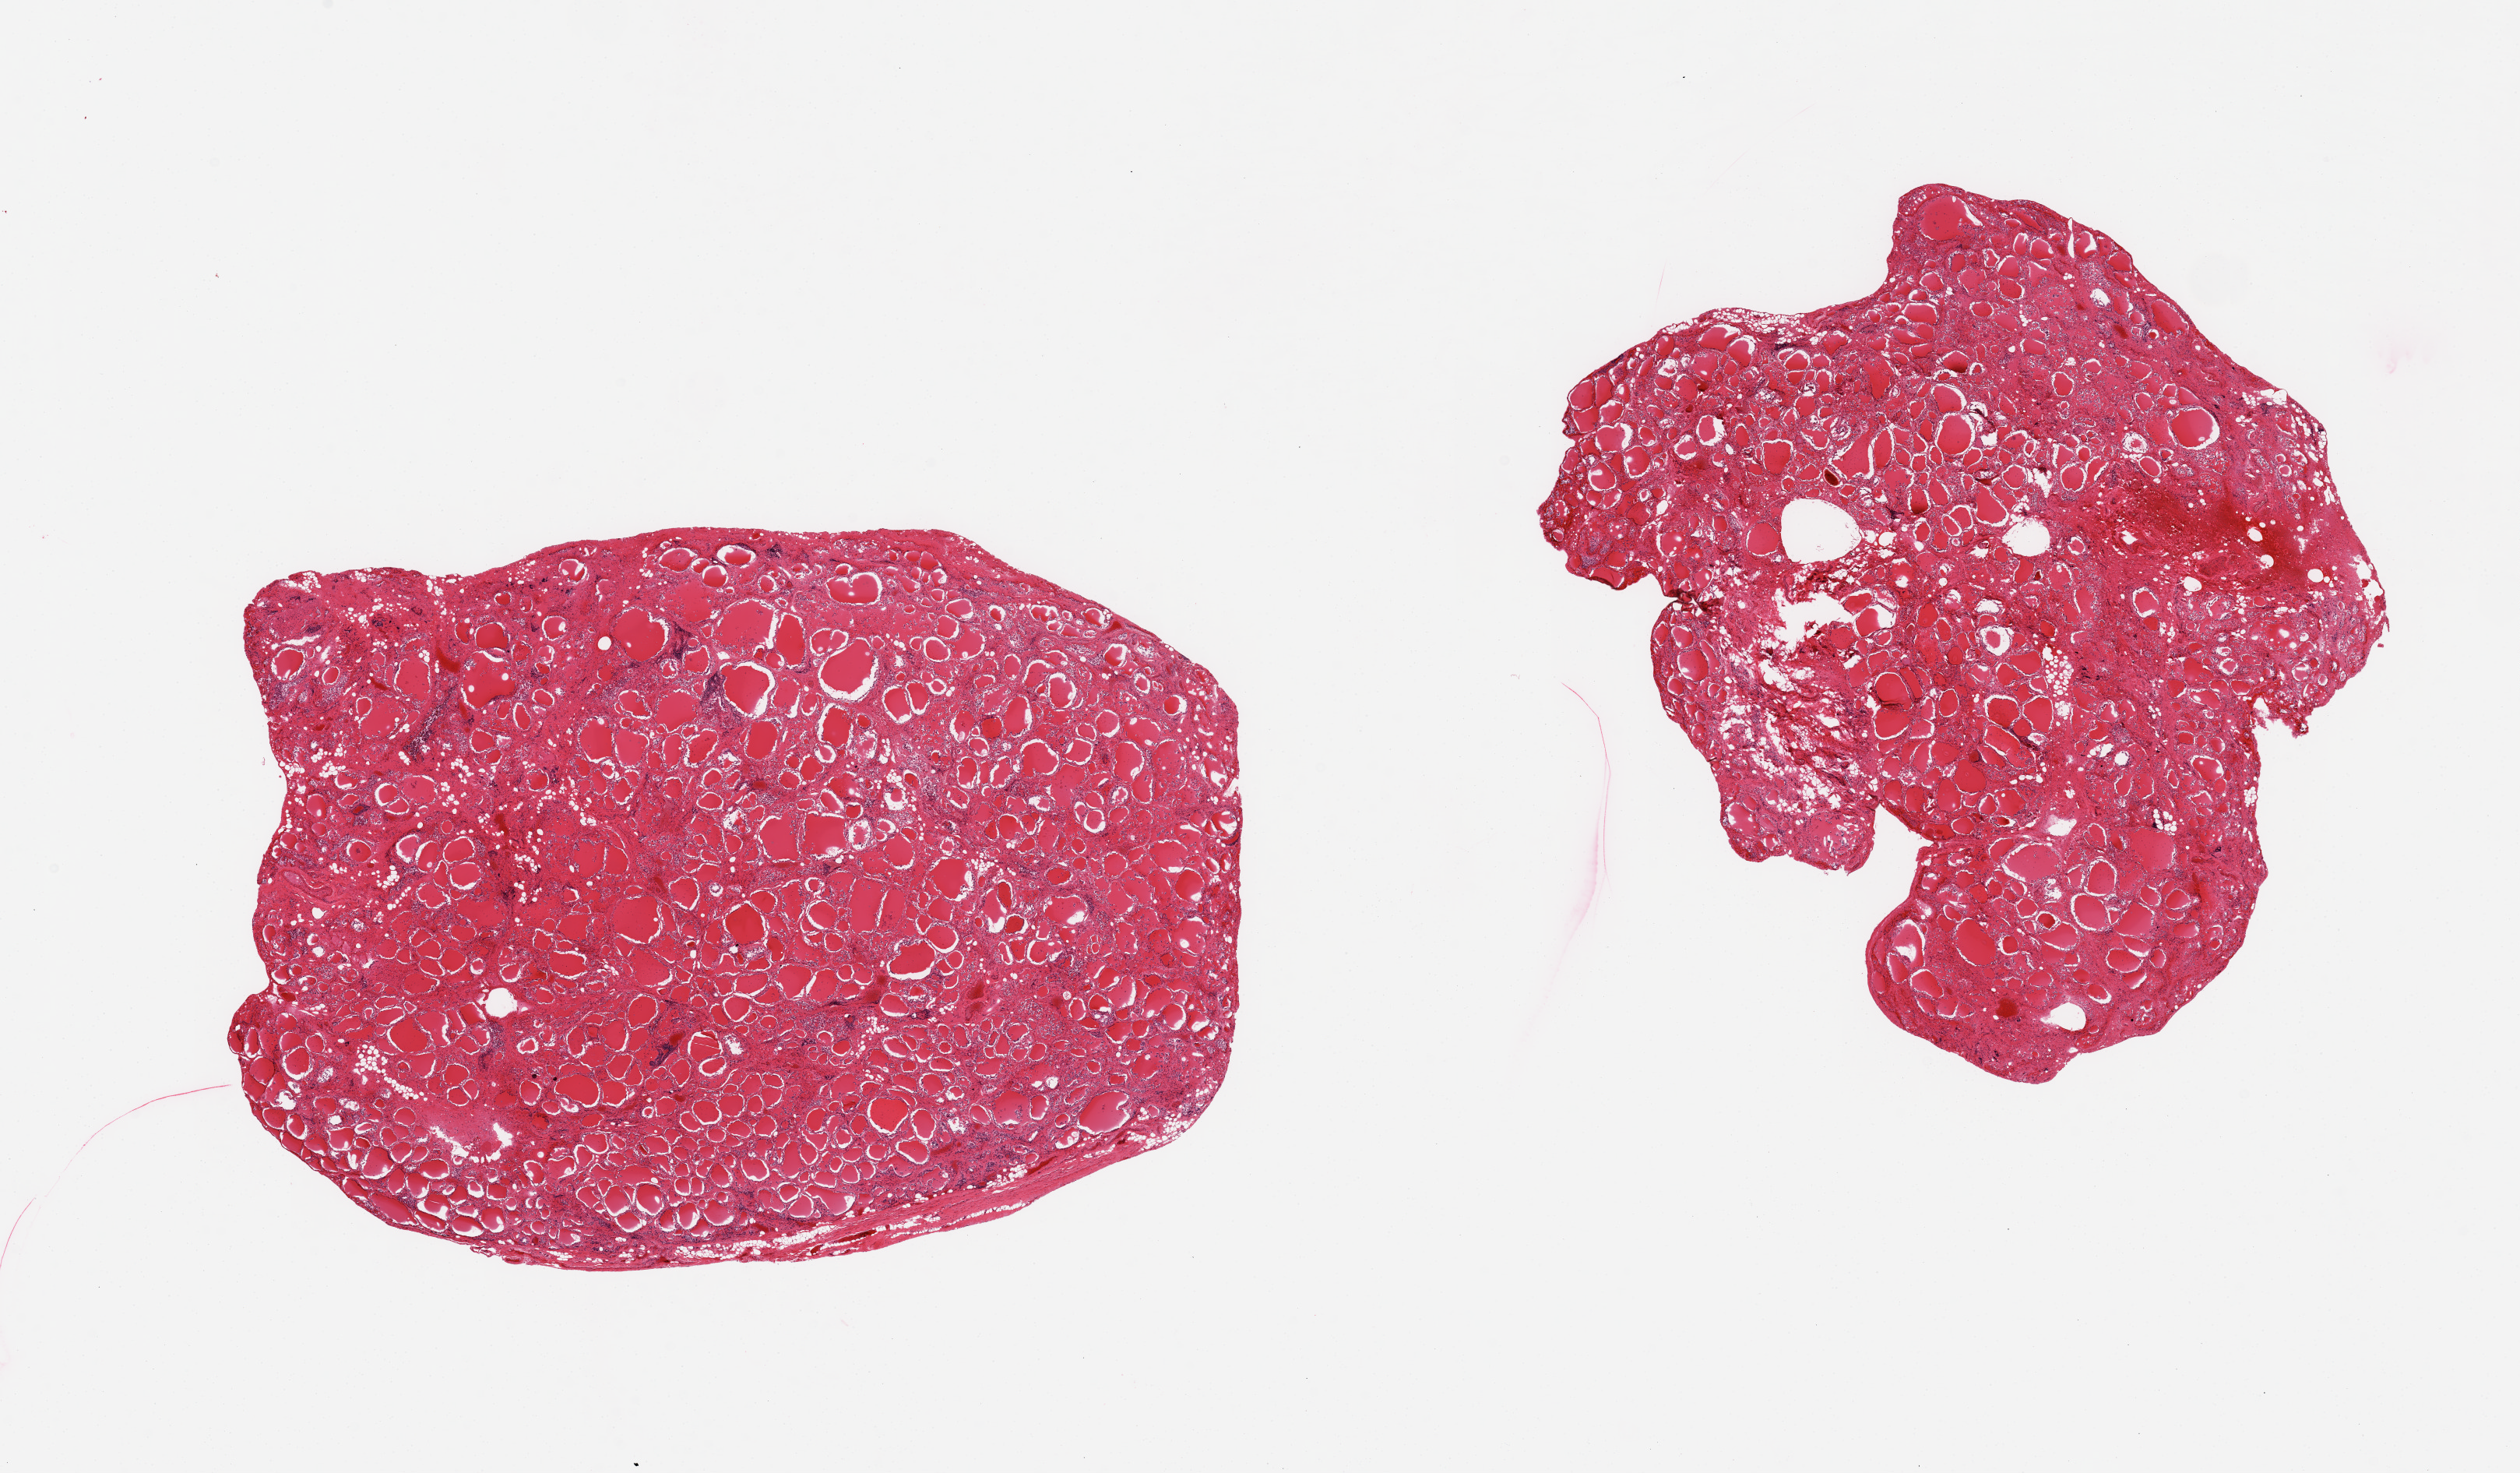
Digitized haematoxylin and eosin-stained section, low-resolution overview of the scanned area, about 25.6 x 15.0 mm (slide scanned at 20x). PAXgene-fixed, paraffin-embedded tissue. Sampled site (target tissue): thyroid. Donor tissue sample. Male donor.
Reviewer comment on this tissue sample: 2 pieces.